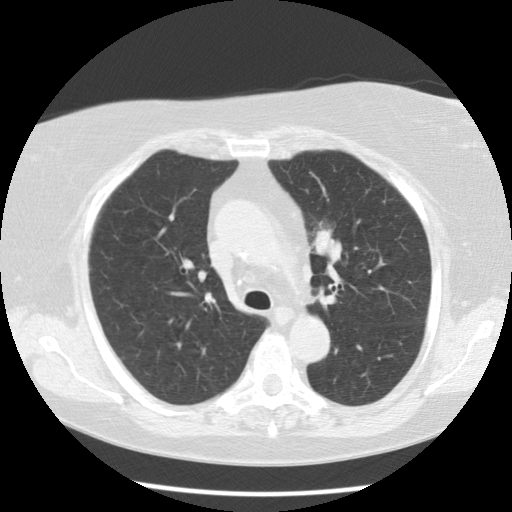
Low-dose screening chest CT, one axial slice. Position 79 of 109 along the scan axis. Reconstruction kernel STANDARD. Lung window (W 1500 / L -600 HU). 2.5 mm slice thickness. 512 × 512 image matrix, field of view 334 × 334 mm.
Structures marked on this image (manually delineated by an expert):
- lesion 1 (tumor, upper lobe of left lung): bounding box (x1, y1, x2, y2) in pixels: (313, 228, 342, 263)